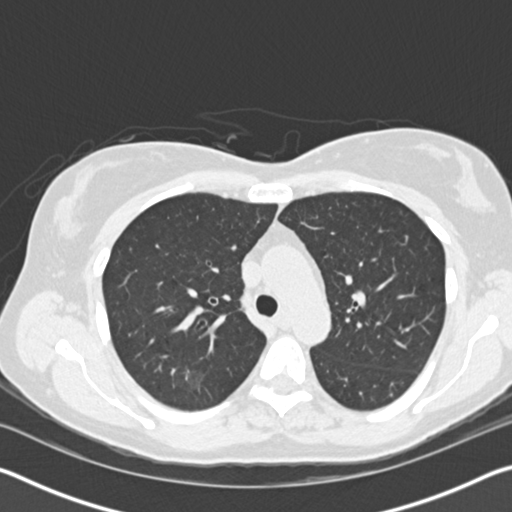
Chest CT (low-dose screening protocol), one axial image; baseline screening round; lung window (W 1500 / L -600 HU); 2 mm slice thickness; standard (soft-tissue) reconstruction kernel (B30f). Female participant, aged 58 years at enrolment. Current smoker at enrolment.
Lesion marked by an expert reader, bounding box <161,347,222,406> (left, top, right, bottom; pixels). The screening reader recorded 3 non-calcified nodules or masses ≥4 mm on this exam (right upper lobe, left upper lobe, left upper lobe); which of them this box marks is not recorded. Official screen result: positive, change unspecified: nodule(s) >= 4 mm or enlarging nodule(s), mass(es), or other non-specific abnormalities suspicious for lung cancer. Later outcome: lung cancer diagnosed 487 days after this screen — bronchiolo-alveolar adenocarcinoma, NOS, right upper lobe, moderately differentiated (G2), stage IA (AJCC 6th edition), 7 mm at pathology.